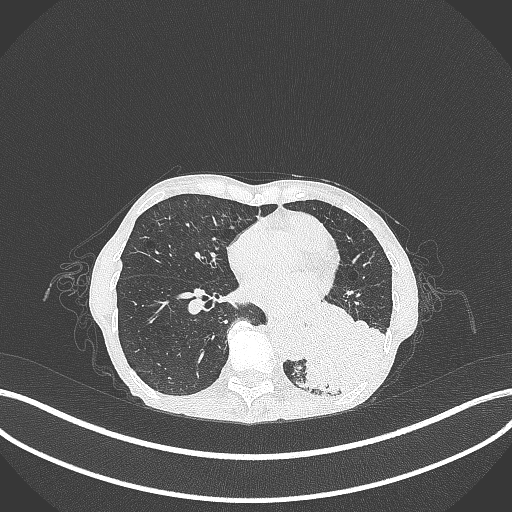
Chest CT, one axial slice; position 106 of 347 along the scan axis; reconstruction kernel B70f; lung window (W 1500 / L -600 HU); 512 × 512 image matrix, field of view 400 × 400 mm. Female patient, age 70 years. From the clinical record (not read from this slice): clinical TNM (as recorded): T3 N0 M0; histopathological grade: G3.
Annotated regions visible in this slice (rectangle marked by the reading radiologist):
- lung tumour (recorded histology: small cell carcinoma): bounding box <290,307,392,397> (left, top, right, bottom; pixels)